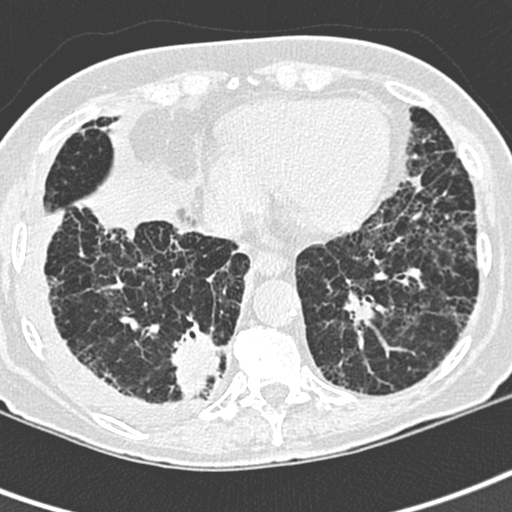
Low-dose screening chest CT, one axial slice; position 84 of 220 along the scan axis; 120 kVp; lung window (W 1500 / L -600 HU); 512 × 512 image matrix.
Annotated regions visible in this slice (expert manual segmentation):
- lesion 1 (tumor, lower lobe of right lung): bounding box <170,318,222,399> (left, top, right, bottom; pixels)